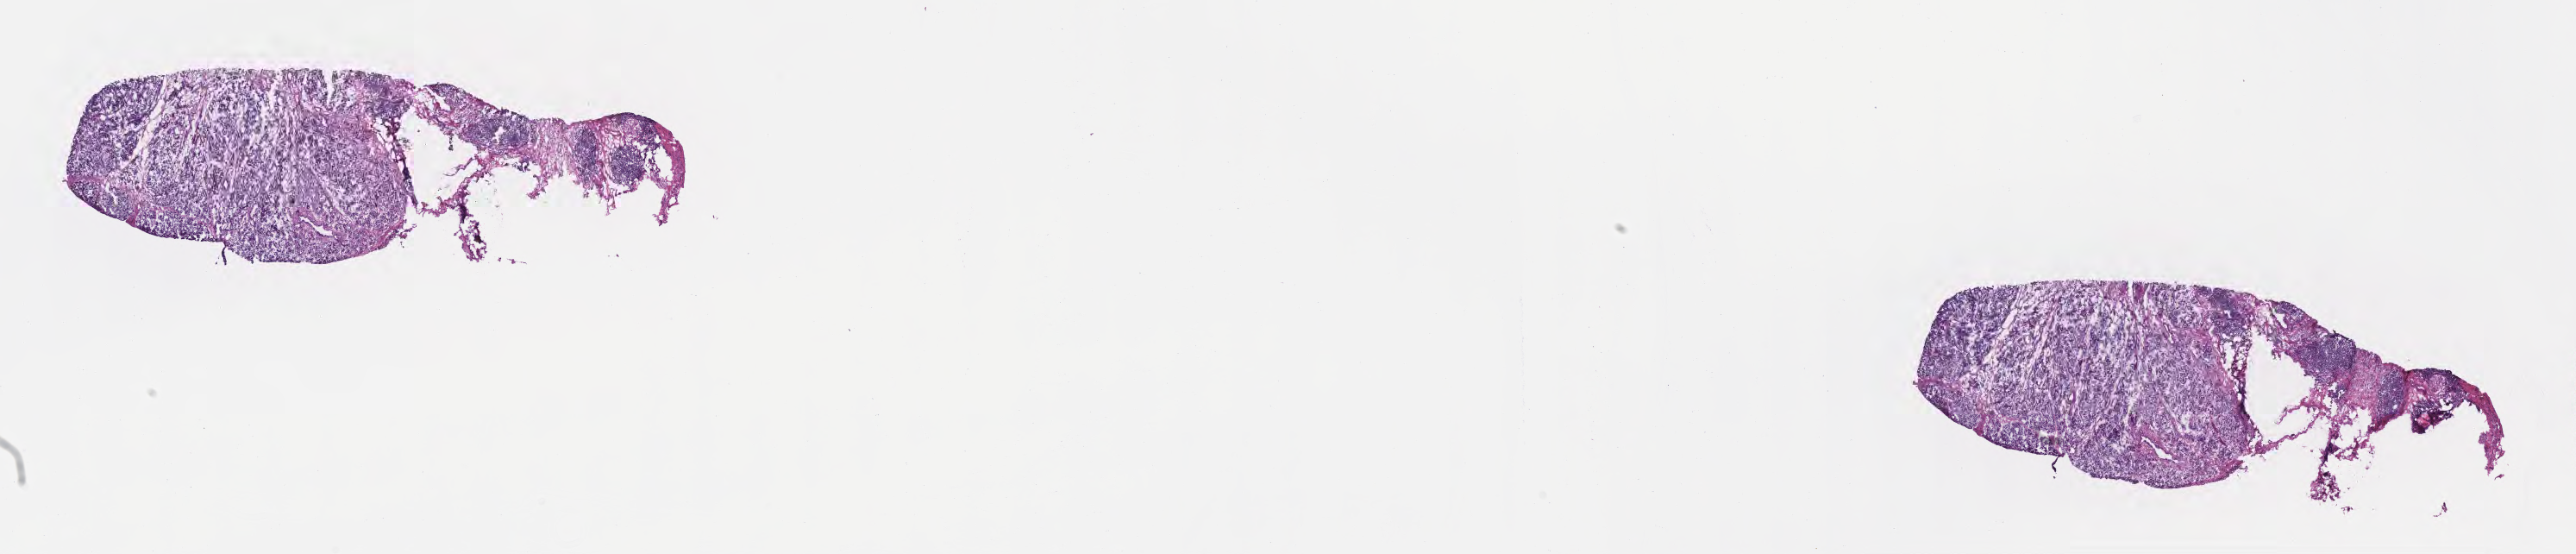
Digitized H&E-stained section, shown as a low-resolution overview of the whole scanned area (about 24.2 x 5.2 mm). Frozen section (tissue freezing medium). Specimen: primary tumor. Anatomic site: head of pancreas. Patient: male, age at initial diagnosis 53 years. Slide review estimates, as recorded: tumor cells 60%, tumor nuclei 60%, stromal cells 38%, necrosis 2%, normal cells 0%. Infiltration values recorded for this section: lymphocyte infiltration 33%, monocyte infiltration 2%, neutrophil infiltration 0%.
* histologic diagnosis: Infiltrating duct carcinoma, NOS
* section: bottom of the tissue portion